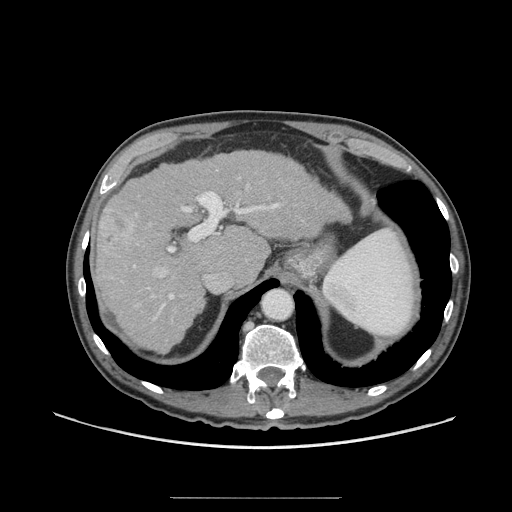
Contrast-enhanced abdominal CT (liver protocol), one axial slice; position 49 of 71 along the scan axis; reconstruction kernel STANDARD; soft-tissue window (W 400 / L 40 HU); 512 × 512 image matrix, field of view 400 × 400 mm. Case-level facts recorded for this patient, not image findings: diagnosis: hepatocellular carcinoma (patient treated with transarterial chemoembolisation; whether this scan precedes or follows treatment is not stated here); TNM stage (as recorded): Stage-I.
Structures marked on this image (semi-automatically segmented with operator editing):
- abdominal aorta: bounding box (x1, y1, x2, y2) in pixels: (263, 290, 292, 319)
- liver parenchyma outside the tumour (the mass and vessels are separate outlines, so this box may not span the whole liver): (96, 150, 348, 350)
- mass: (97, 204, 140, 260)
- liver vessels: (133, 197, 279, 321)